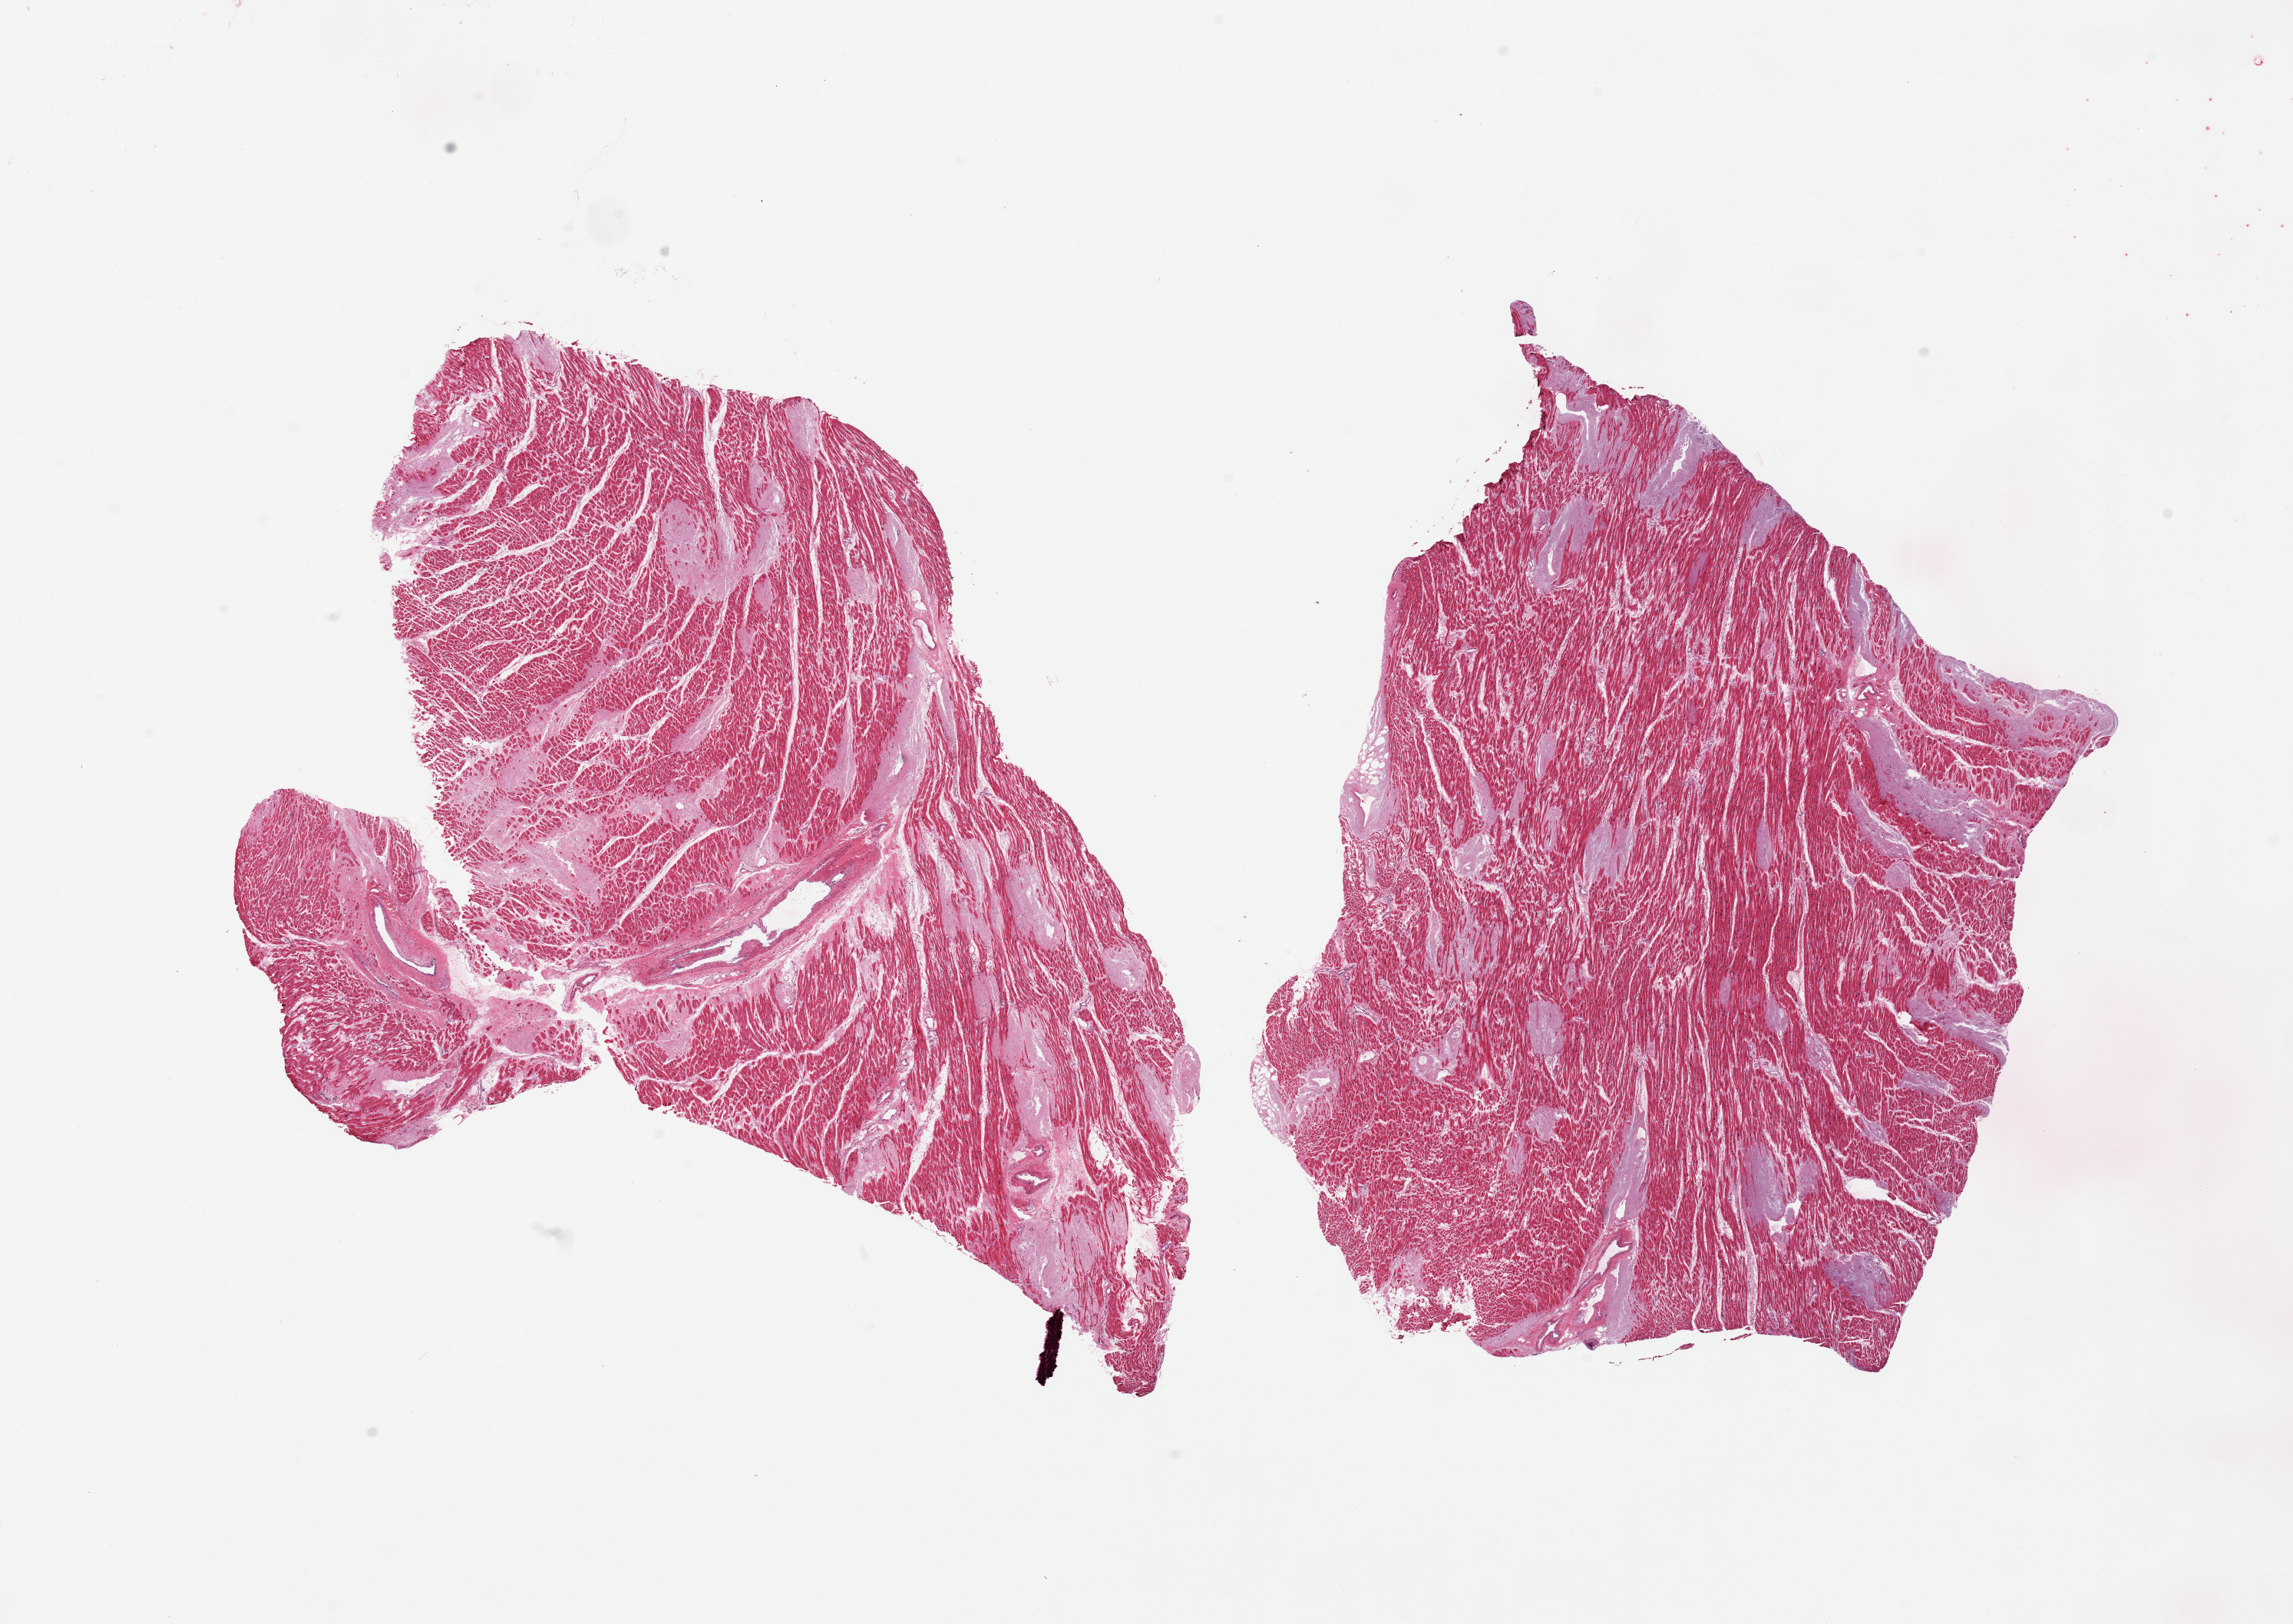
Whole-slide image, H&E stain, a low-resolution overview of the entire scanned area, about 23.6 x 16.7 mm (slide scanned at 20x), PAXgene-fixed, paraffin-embedded tissue, sampled site (target tissue): heart, donor tissue sample. Male donor.
Reviewer comment on this tissue sample: 2 pieces, diffuse inflitrative process consistent with amyloid.